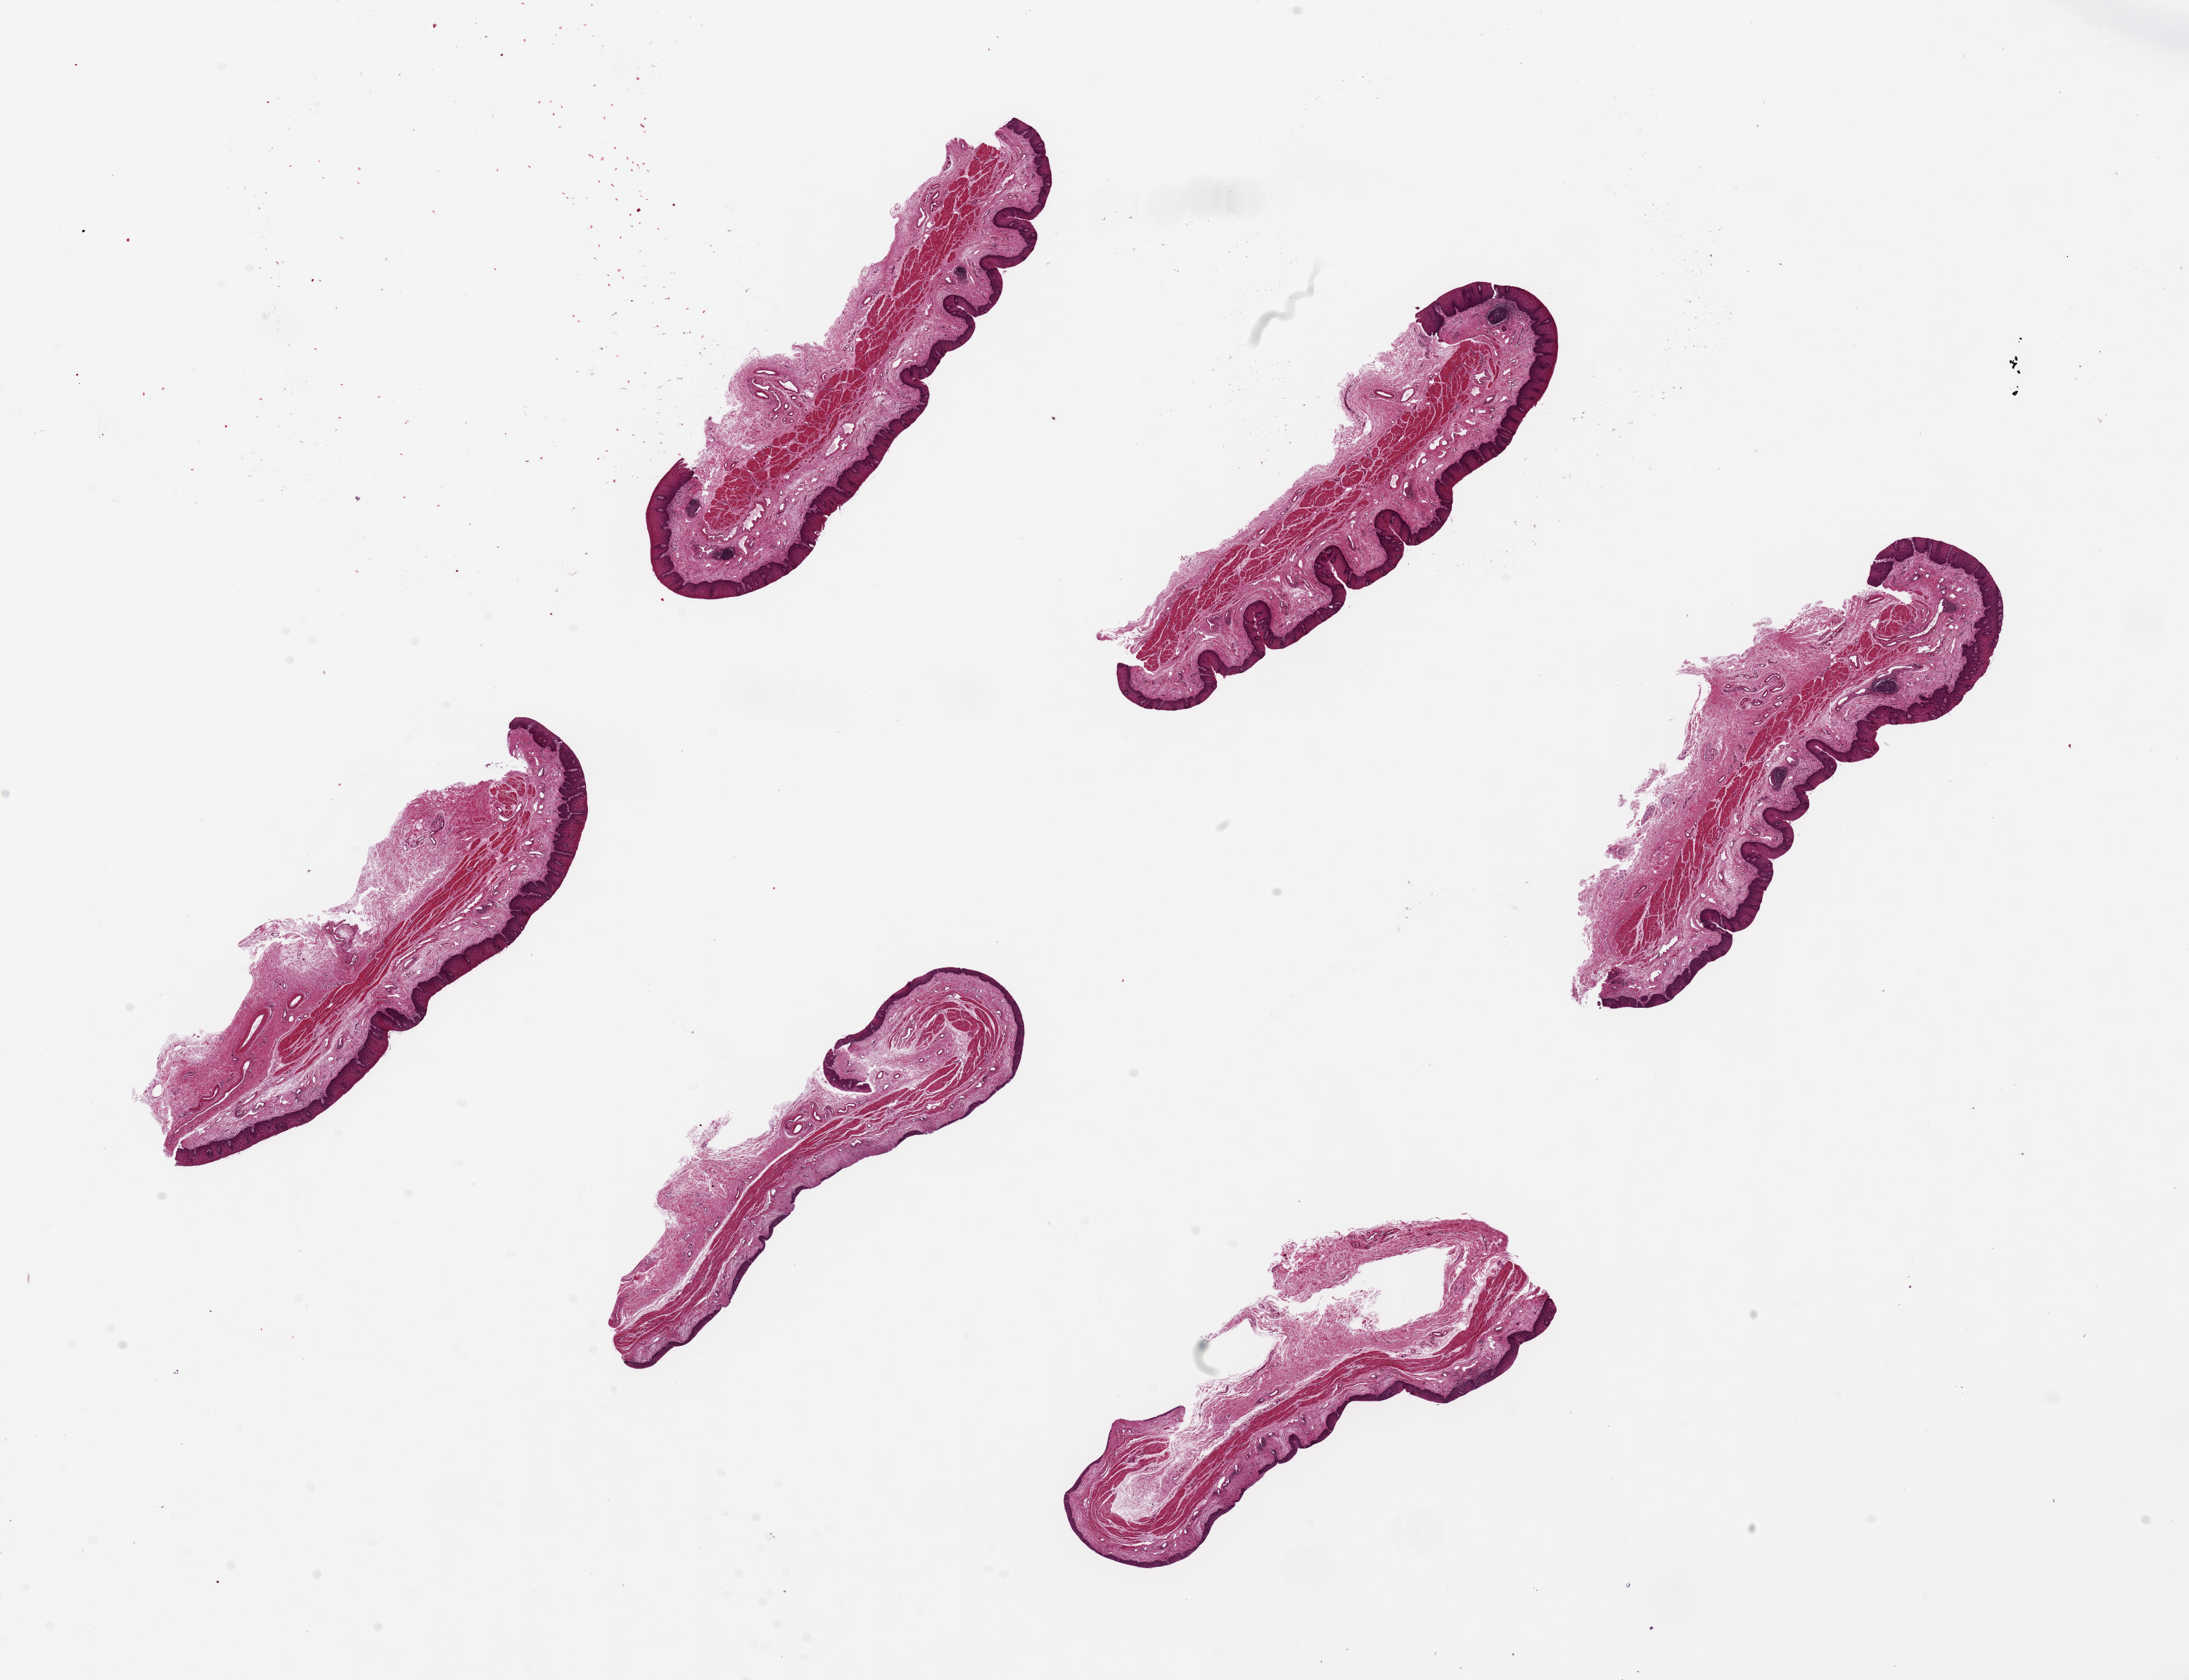
Whole-slide image, haematoxylin and eosin stain, brightfield, whole scanned area (about 24.6 x 18.9 mm, acquisition: 20x scan) shown as a low-resolution overview, PAXgene-fixed paraffin-embedded (PFPE) section, sampled site (target tissue): esophageal mucous membrane, tissue donor sample. Donor: male.
Reviewer comment on this tissue sample: 6 pieces ~6x1.5mm. Squamous mucosa is ~10% thickness.